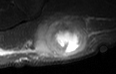
MRI of an extremity soft-tissue mass, one axial slice; slice 22 of 36 in the series (ordered by position); STIR; MR volume resampled by the dataset authors to the PET/CT grid (not the native acquisition matrix); 116 × 74 image matrix. Male patient. Case-level facts recorded for this patient, not image findings: histological type: pleiomorphic leiomyosarcoma; grade: high; site of the primary tumour: left buttock.
Outlined on this slice (expert contour drawn on MRI and transferred to this co-registered scan by the dataset authors):
- gross tumour volume including surrounding oedema: bounding box <32,19,81,57> (left, top, right, bottom; pixels)
- gross tumour volume (mass): <32,21,81,56>